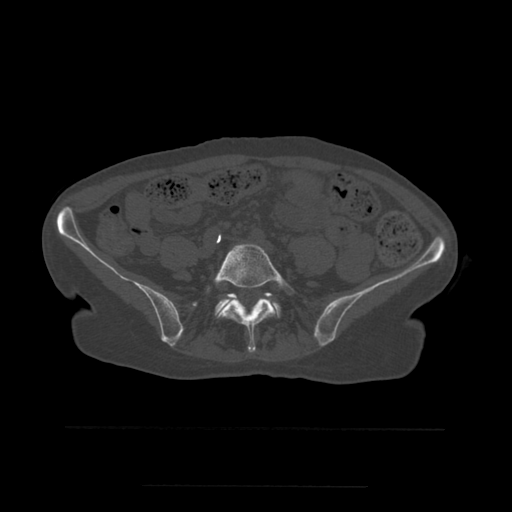
CT including the spine, one axial slice; slice 143 of 544 in the series (ordered by position); bone window (W 1800 / L 400 HU); 1.25 mm slice thickness; 512 × 512 image matrix. Patient age 58 years. From the clinical record (not read from this slice): primary cancer: lung.
Annotated regions visible in this slice (semi-automatically segmented with operator editing):
- L5 vertebra: bounding box <208,244,294,353> (left, top, right, bottom; pixels)